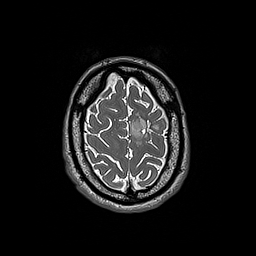
Brain MRI from a brain-tumour surgery series, one axial slice; position 44 of 192 along the scan axis; 1 mm slice thickness; 256 × 256 image matrix. Case-level facts recorded for this patient, not image findings: histopathology: Oligodendroglioma; WHO grade: 3; IDH mutation: yes; tumour location: Left Frontal.
Structures marked on this image (outlined manually by an expert reader):
- tumour: box from (x=131, y=116) to (x=159, y=146) px